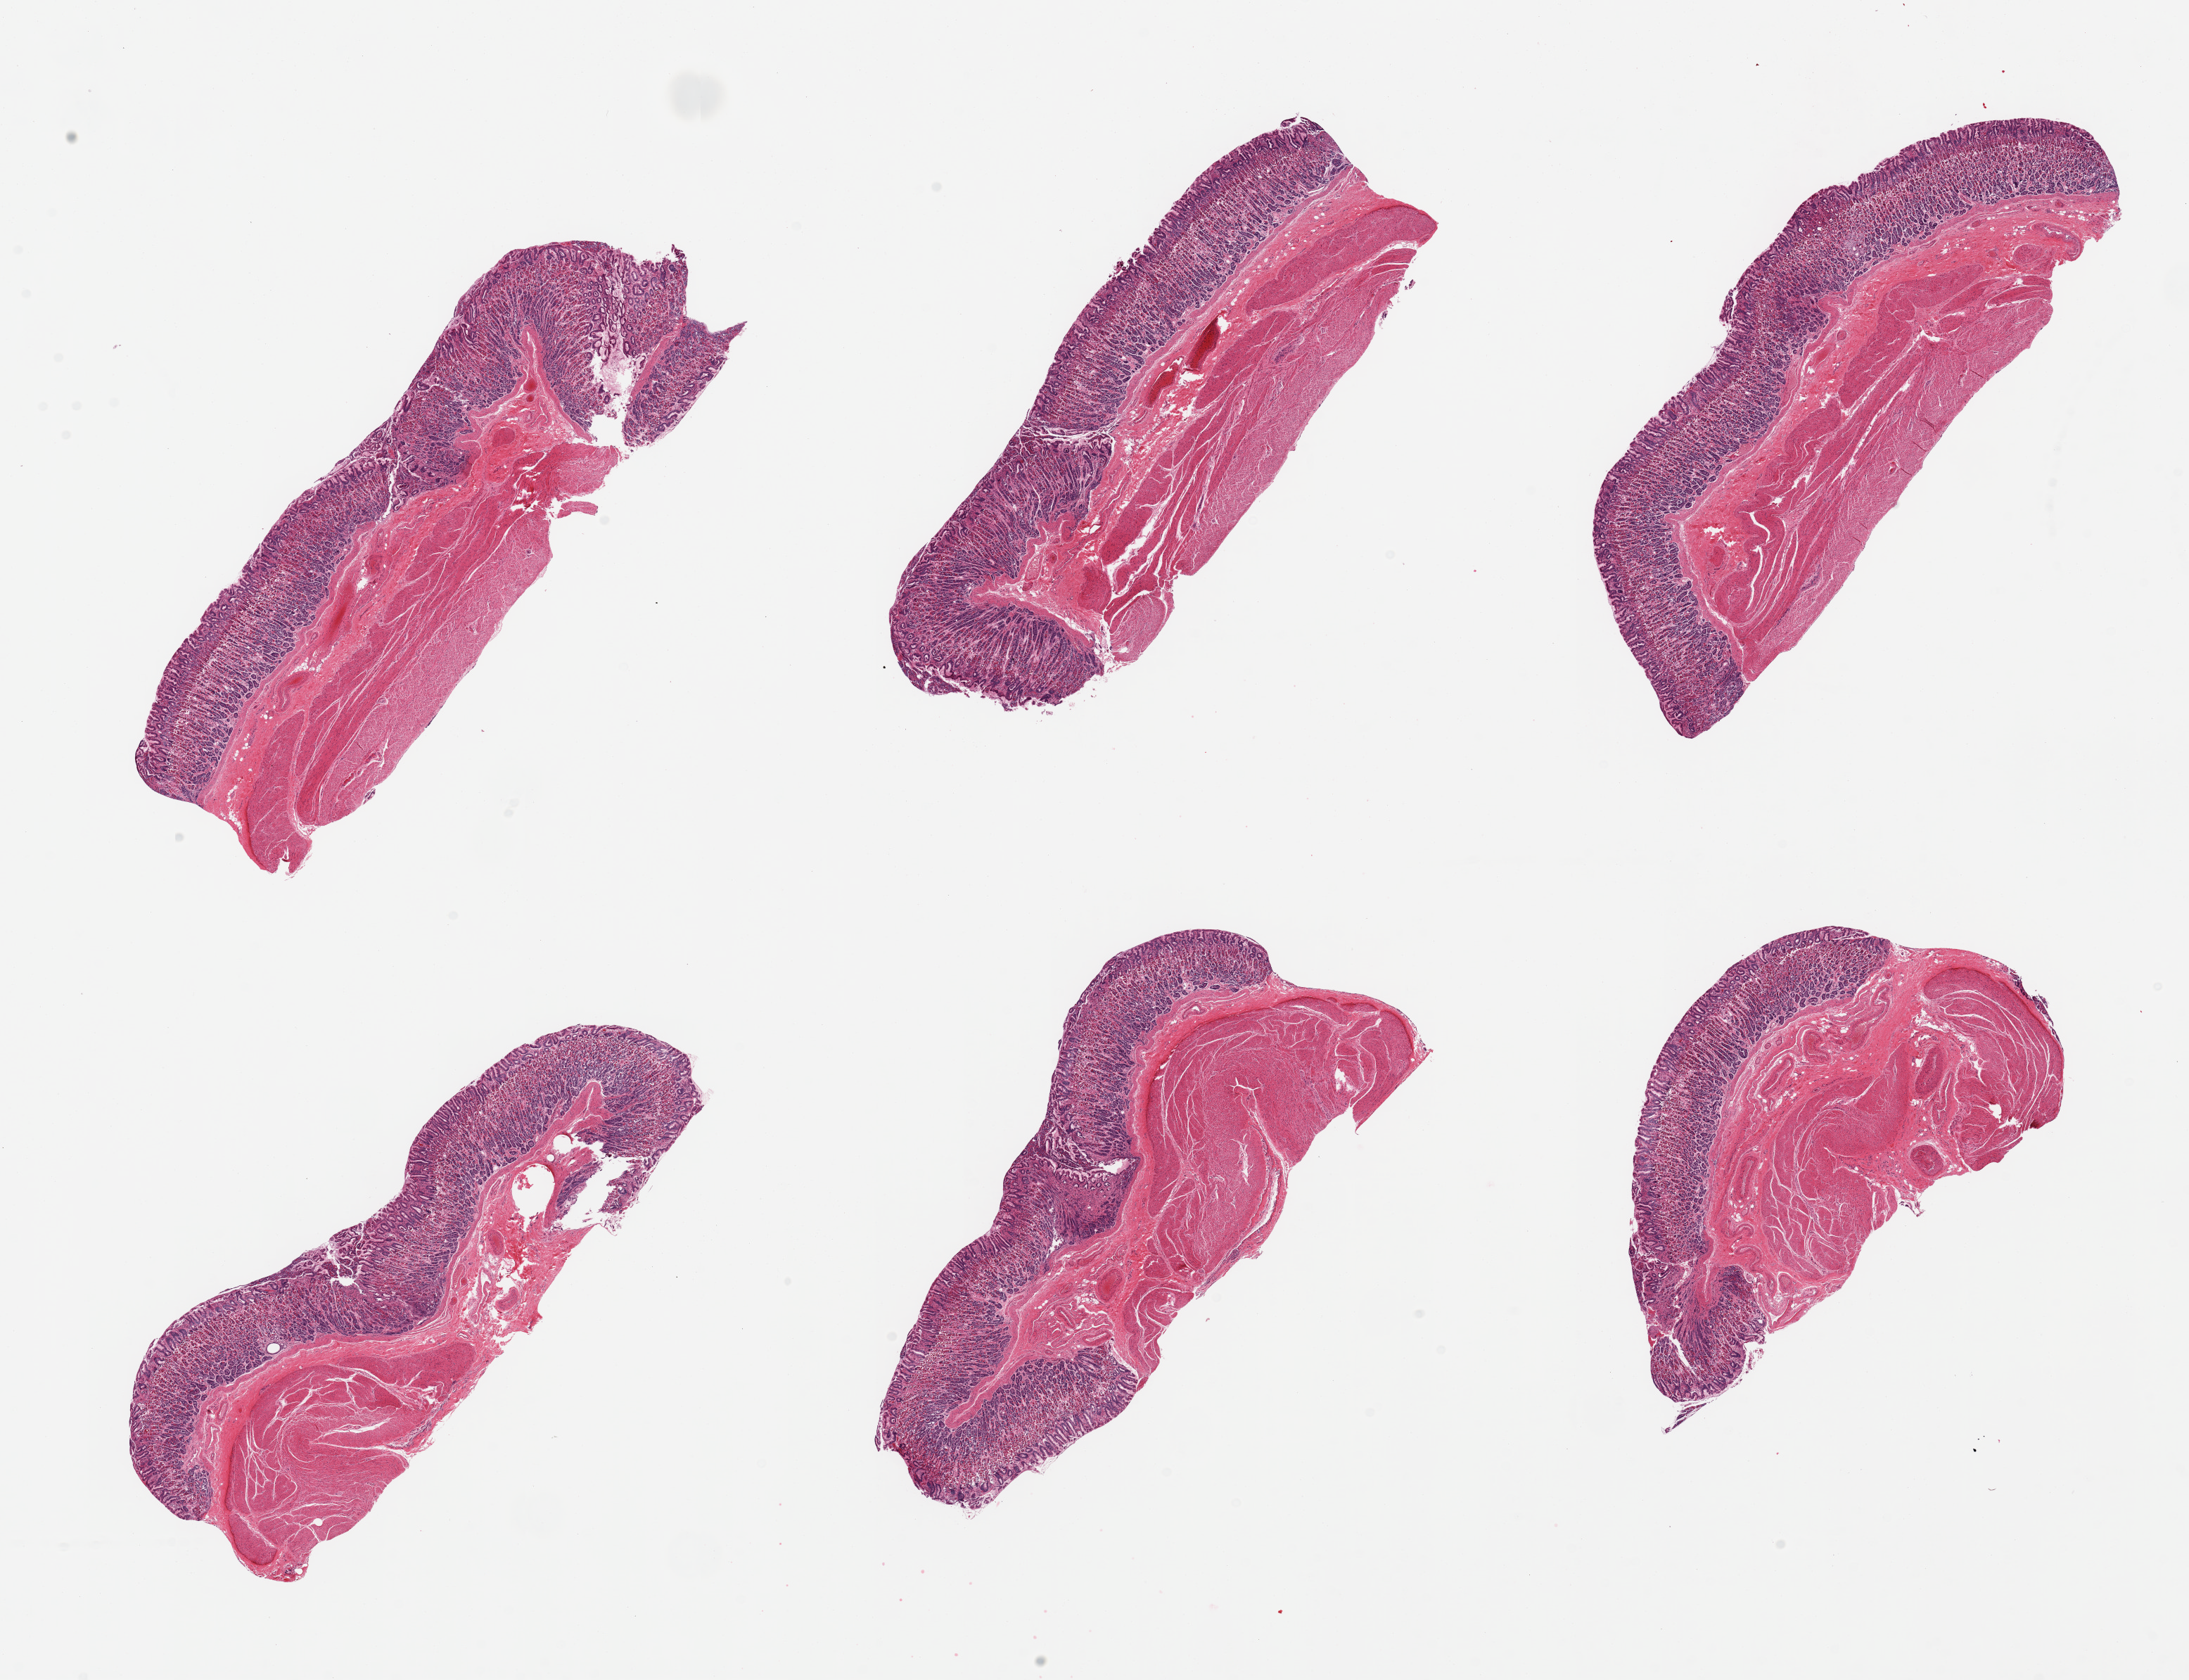
Hematoxylin and eosin (H&E) whole-slide image — low-resolution overview of the scanned area, about 24.6 x 18.9 mm; PAXgene-fixed paraffin-embedded (PFPE) section; sampled site (target tissue): stomach; donor tissue sample.
- review note (as recorded): 6 pieces; congestion; essentially well preserved full thickness sections